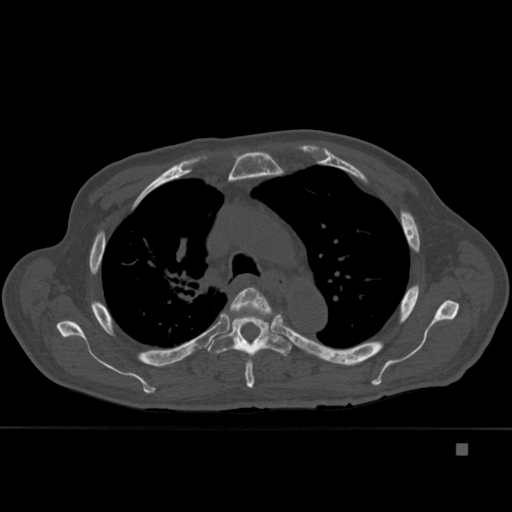
CT including the spine, one axial slice. Slice 312 of 451 in the series (ordered by position). Bone window (W 1800 / L 400 HU). 1.5 mm slice thickness. 512 × 512 image matrix, field of view 378 × 378 mm. Male patient, age 75 years. From the clinical record (not read from this slice): primary cancer: prostate.
Annotated regions visible in this slice (semi-automatic segmentation, software-assisted and operator-edited):
- T4 vertebra: bounding box (x1, y1, x2, y2) in pixels: (230, 287, 279, 388)
- T5 vertebra: (208, 310, 292, 363)